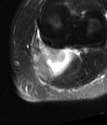
MRI of an extremity soft-tissue mass, one axial slice; slice 50 of 78 in the series (ordered by position); T2-weighted fat-saturated; MR volume resampled by the dataset authors to the PET/CT grid (not the native acquisition matrix); 3.27 mm slice thickness; 107 × 125 image matrix, field of view 104 × 122 mm. Female patient. From the clinical record (not read from this slice): histological type: extraskeletal high grade osteogenic sarcoma; grade: high; site of the primary tumour: left calf.
Annotated regions visible in this slice (expert contour drawn on MRI and transferred to this co-registered scan by the dataset authors):
- gross tumour volume (mass): bounding box <35,50,74,78> (left, top, right, bottom; pixels)